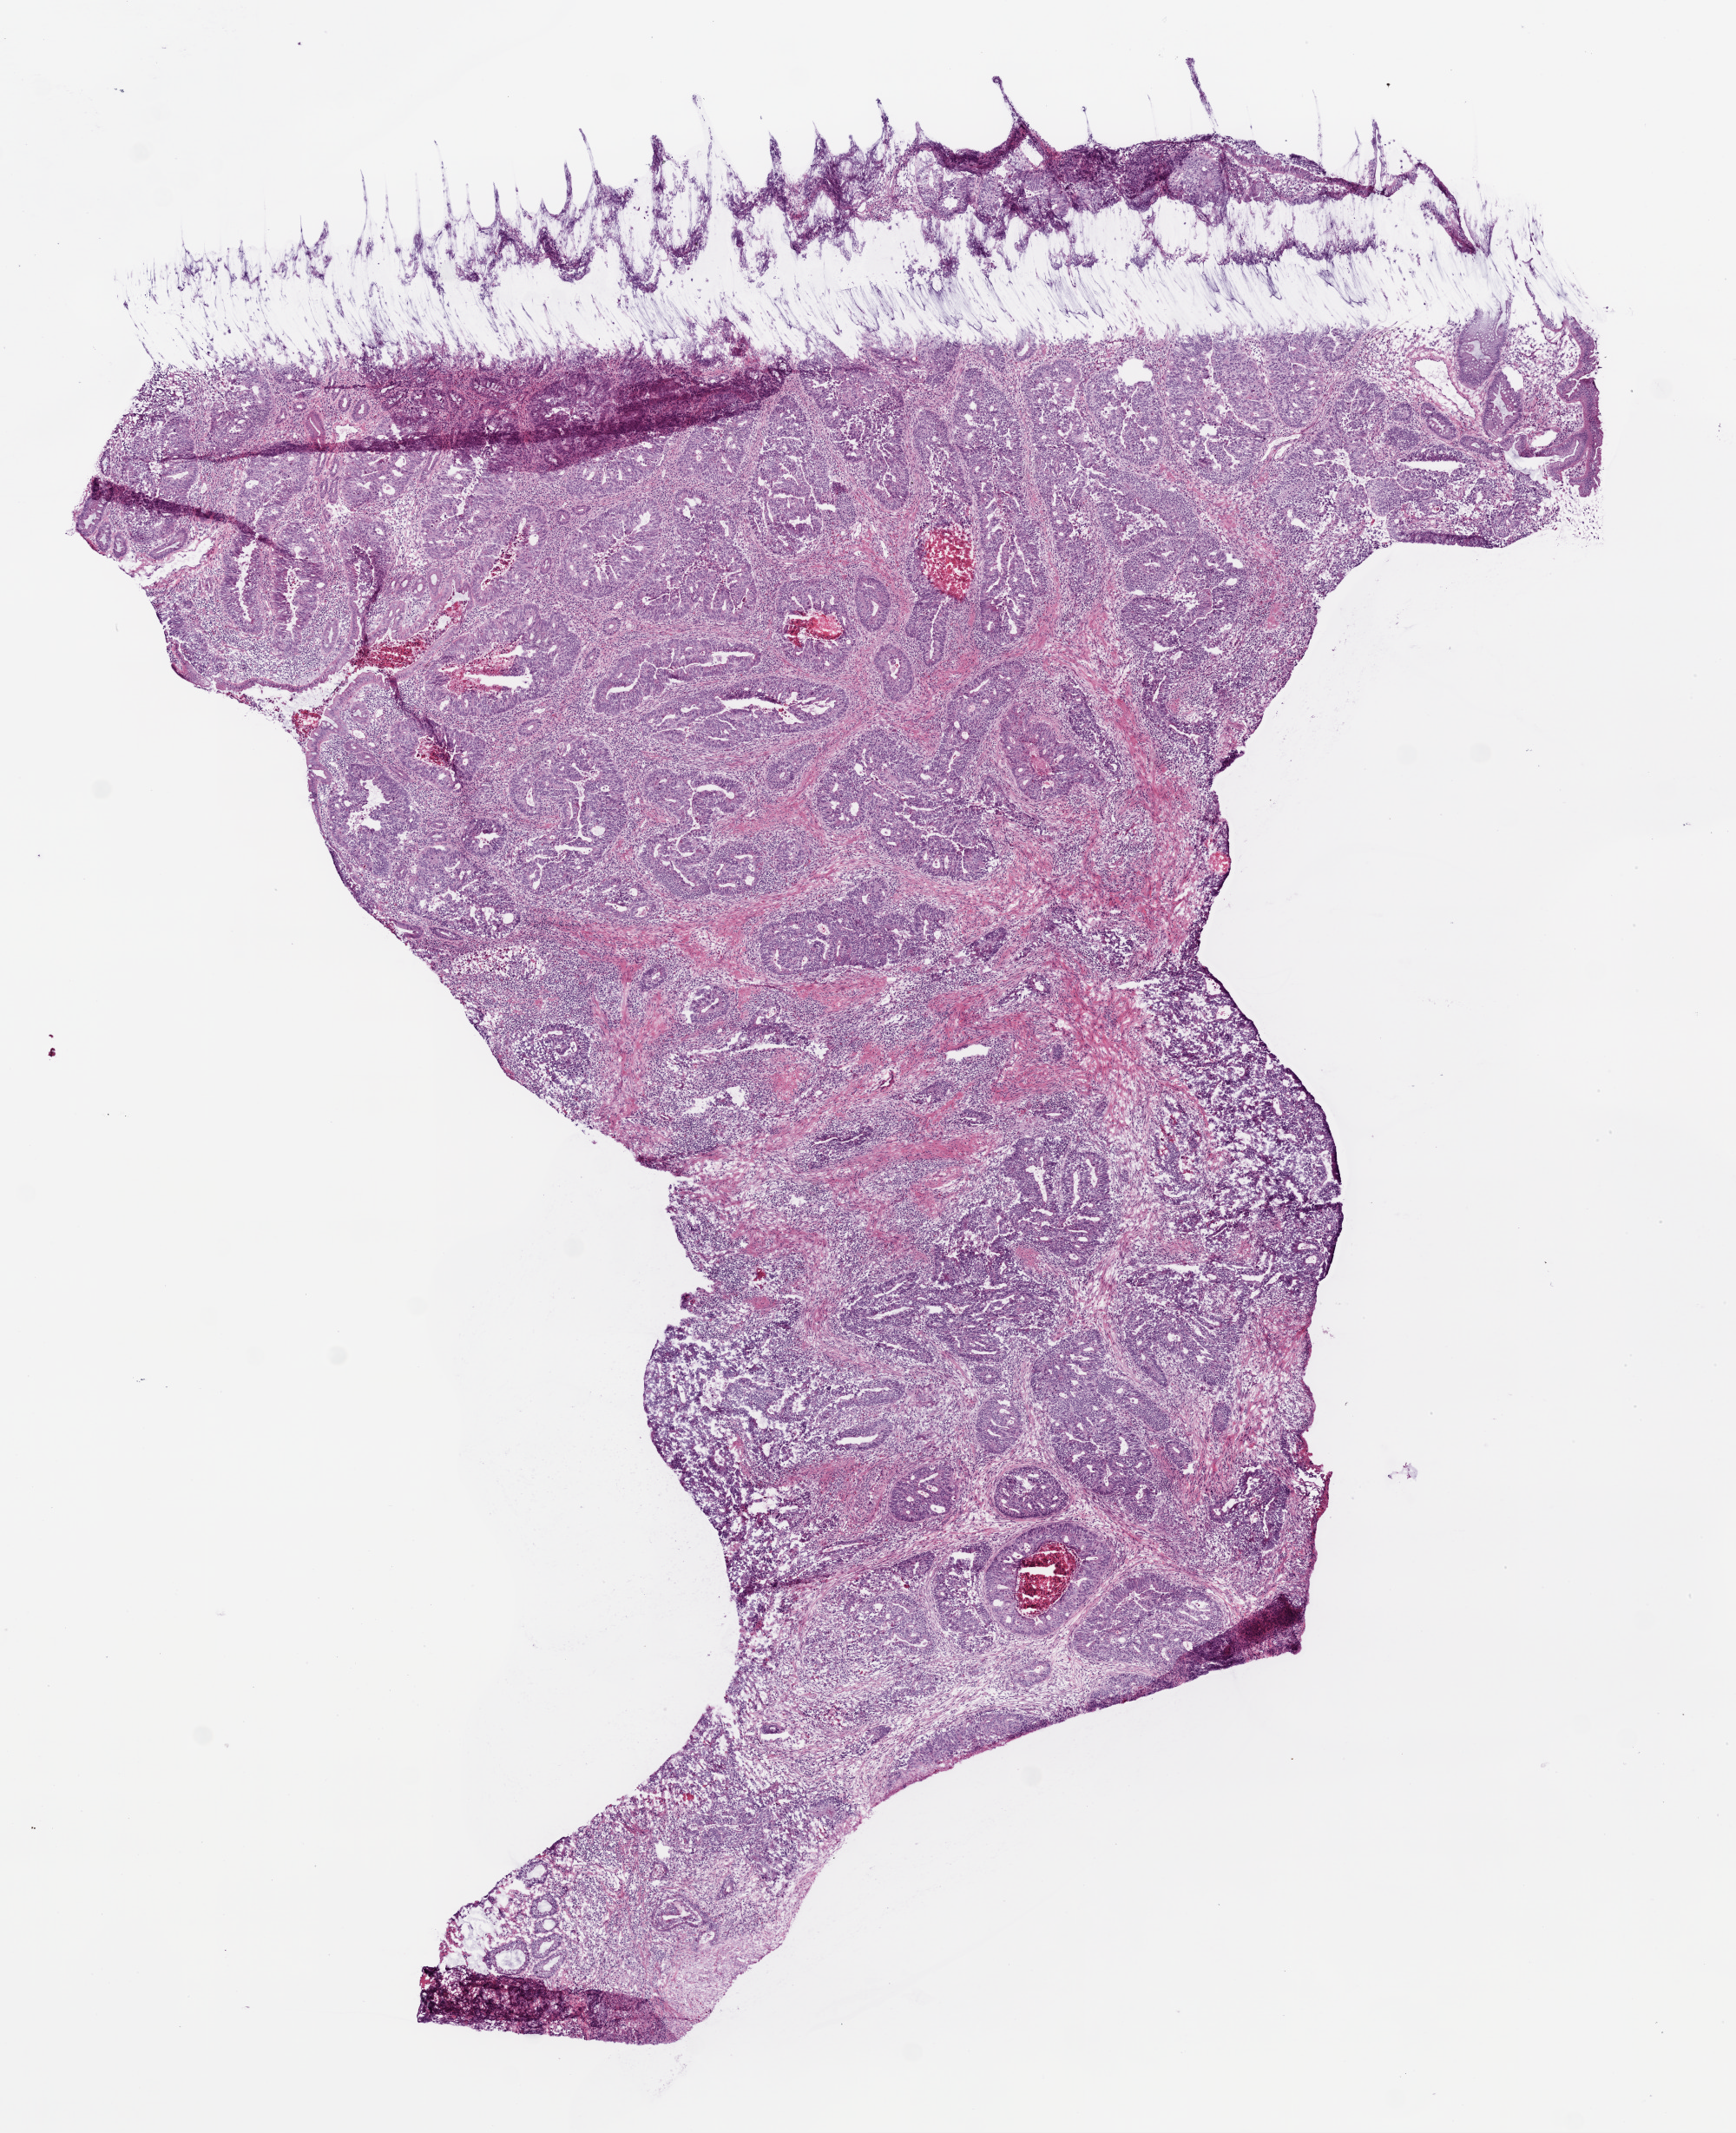
Digitized H&E-stained tissue section (whole slide) — whole scanned area (about 8.0 x 9.9 mm) shown as a low-resolution overview. Frozen section. Colon, primary tumour sample. Male, age 75 years at initial diagnosis. Composition of this section per pathologist review: tumour cells 88%, tumour nuclei 80%, normal cells 0%, stromal cells 10%, necrosis 2%. Inflammatory infiltration, as recorded: lymphocyte infiltration 5%.
AJCC pathologic stage: IIIB (6th edition). Lymph nodes positive (case pathology): 3 of 13 examined. Diagnosis: Adenocarcinoma, NOS.